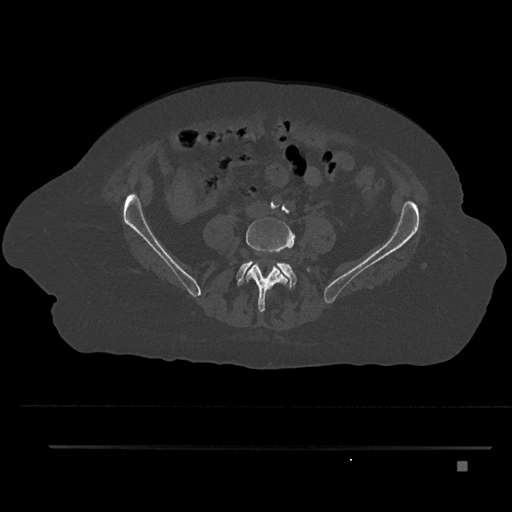
CT including the spine, one axial slice. Bone window (W 1800 / L 400 HU). 0.5 mm slice thickness. 512 × 512 image matrix. Patient: female, 76 years. Case-level facts recorded for this patient, not image findings: primary cancer: lung; vertebrae with lytic lesions (as recorded): T11, L3.
Annotated regions visible in this slice (semi-automatic segmentation, software-assisted and operator-edited):
- L4 vertebra: bounding box [x1, y1, x2, y2] px = [246, 217, 294, 312]
- L5 vertebra: [237, 262, 297, 289]